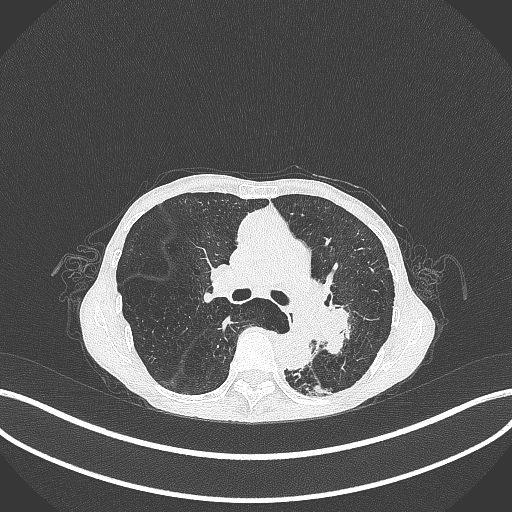
Chest CT, one axial slice; position 170 of 347 along the scan axis; reconstruction kernel B70f; lung window (W 1500 / L -600 HU); 1 mm slice thickness; 512 × 512 image matrix, field of view 400 × 400 mm. Patient: female, 70 years. From the clinical record (not read from this slice): clinical TNM (as recorded): T3 N0 M0.
Outlined on this slice (bounding box drawn by a radiologist):
- lung tumour (recorded histology: small cell carcinoma): bounding box [x1, y1, x2, y2] px = [313, 301, 367, 378]